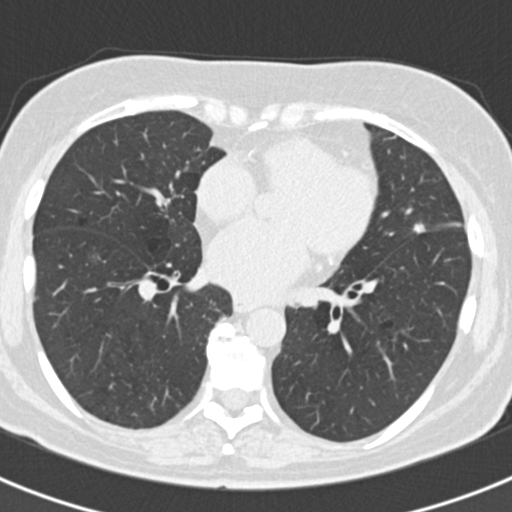
Low-dose screening chest CT, axial slice. Baseline screening round. Lung window (W 1500 / L -600 HU). 2 mm slice thickness. Standard (soft-tissue) reconstruction kernel (B30f). 120 kVp. 512 × 512 image matrix. Female, age 60 years at enrolment. Current smoker at enrolment.
- Expert-annotated lung lesion, bounding box (x1, y1, x2, y2) in pixels: (399, 215, 438, 248).
- The screening reader recorded 3 non-calcified nodules or masses ≥4 mm on this exam; which of them this box marks is not recorded.
- Participant outcome: lung cancer diagnosed 886 days after this screen — non-small cell carcinoma, left upper lobe, poorly differentiated (G3), stage IB (AJCC 6th edition), 7 mm at pathology.